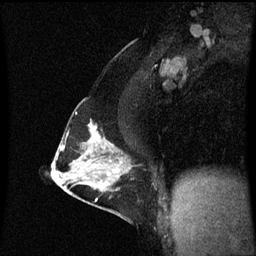
Breast MRI (dynamic contrast-enhanced), one sagittal slice; position 35 of 60 along the scan axis; dynamic contrast-enhanced series, image 2 of 3 at this slice position (ordered by acquisition); 1.5 T; TE 4.2 ms, TR 8.9 ms; 2 mm slice thickness; 256 × 256 image matrix. Female patient, age 47 years. Case-level facts recorded for this patient, not image findings: setting: breast cancer imaged before/during neoadjuvant chemotherapy; receptor status: HR-positive, HER2-negative.
Annotated regions visible in this slice (semi-automatically segmented with operator editing):
- analysis volume of interest (the breast-tissue region the enhancement analysis was run in; not a lesion): bounding box <53,110,134,209> (left, top, right, bottom; pixels)
- tumour enhancement mask (voxels above the 70 % enhancement threshold inside the analysis volume of interest): <73,124,108,163>